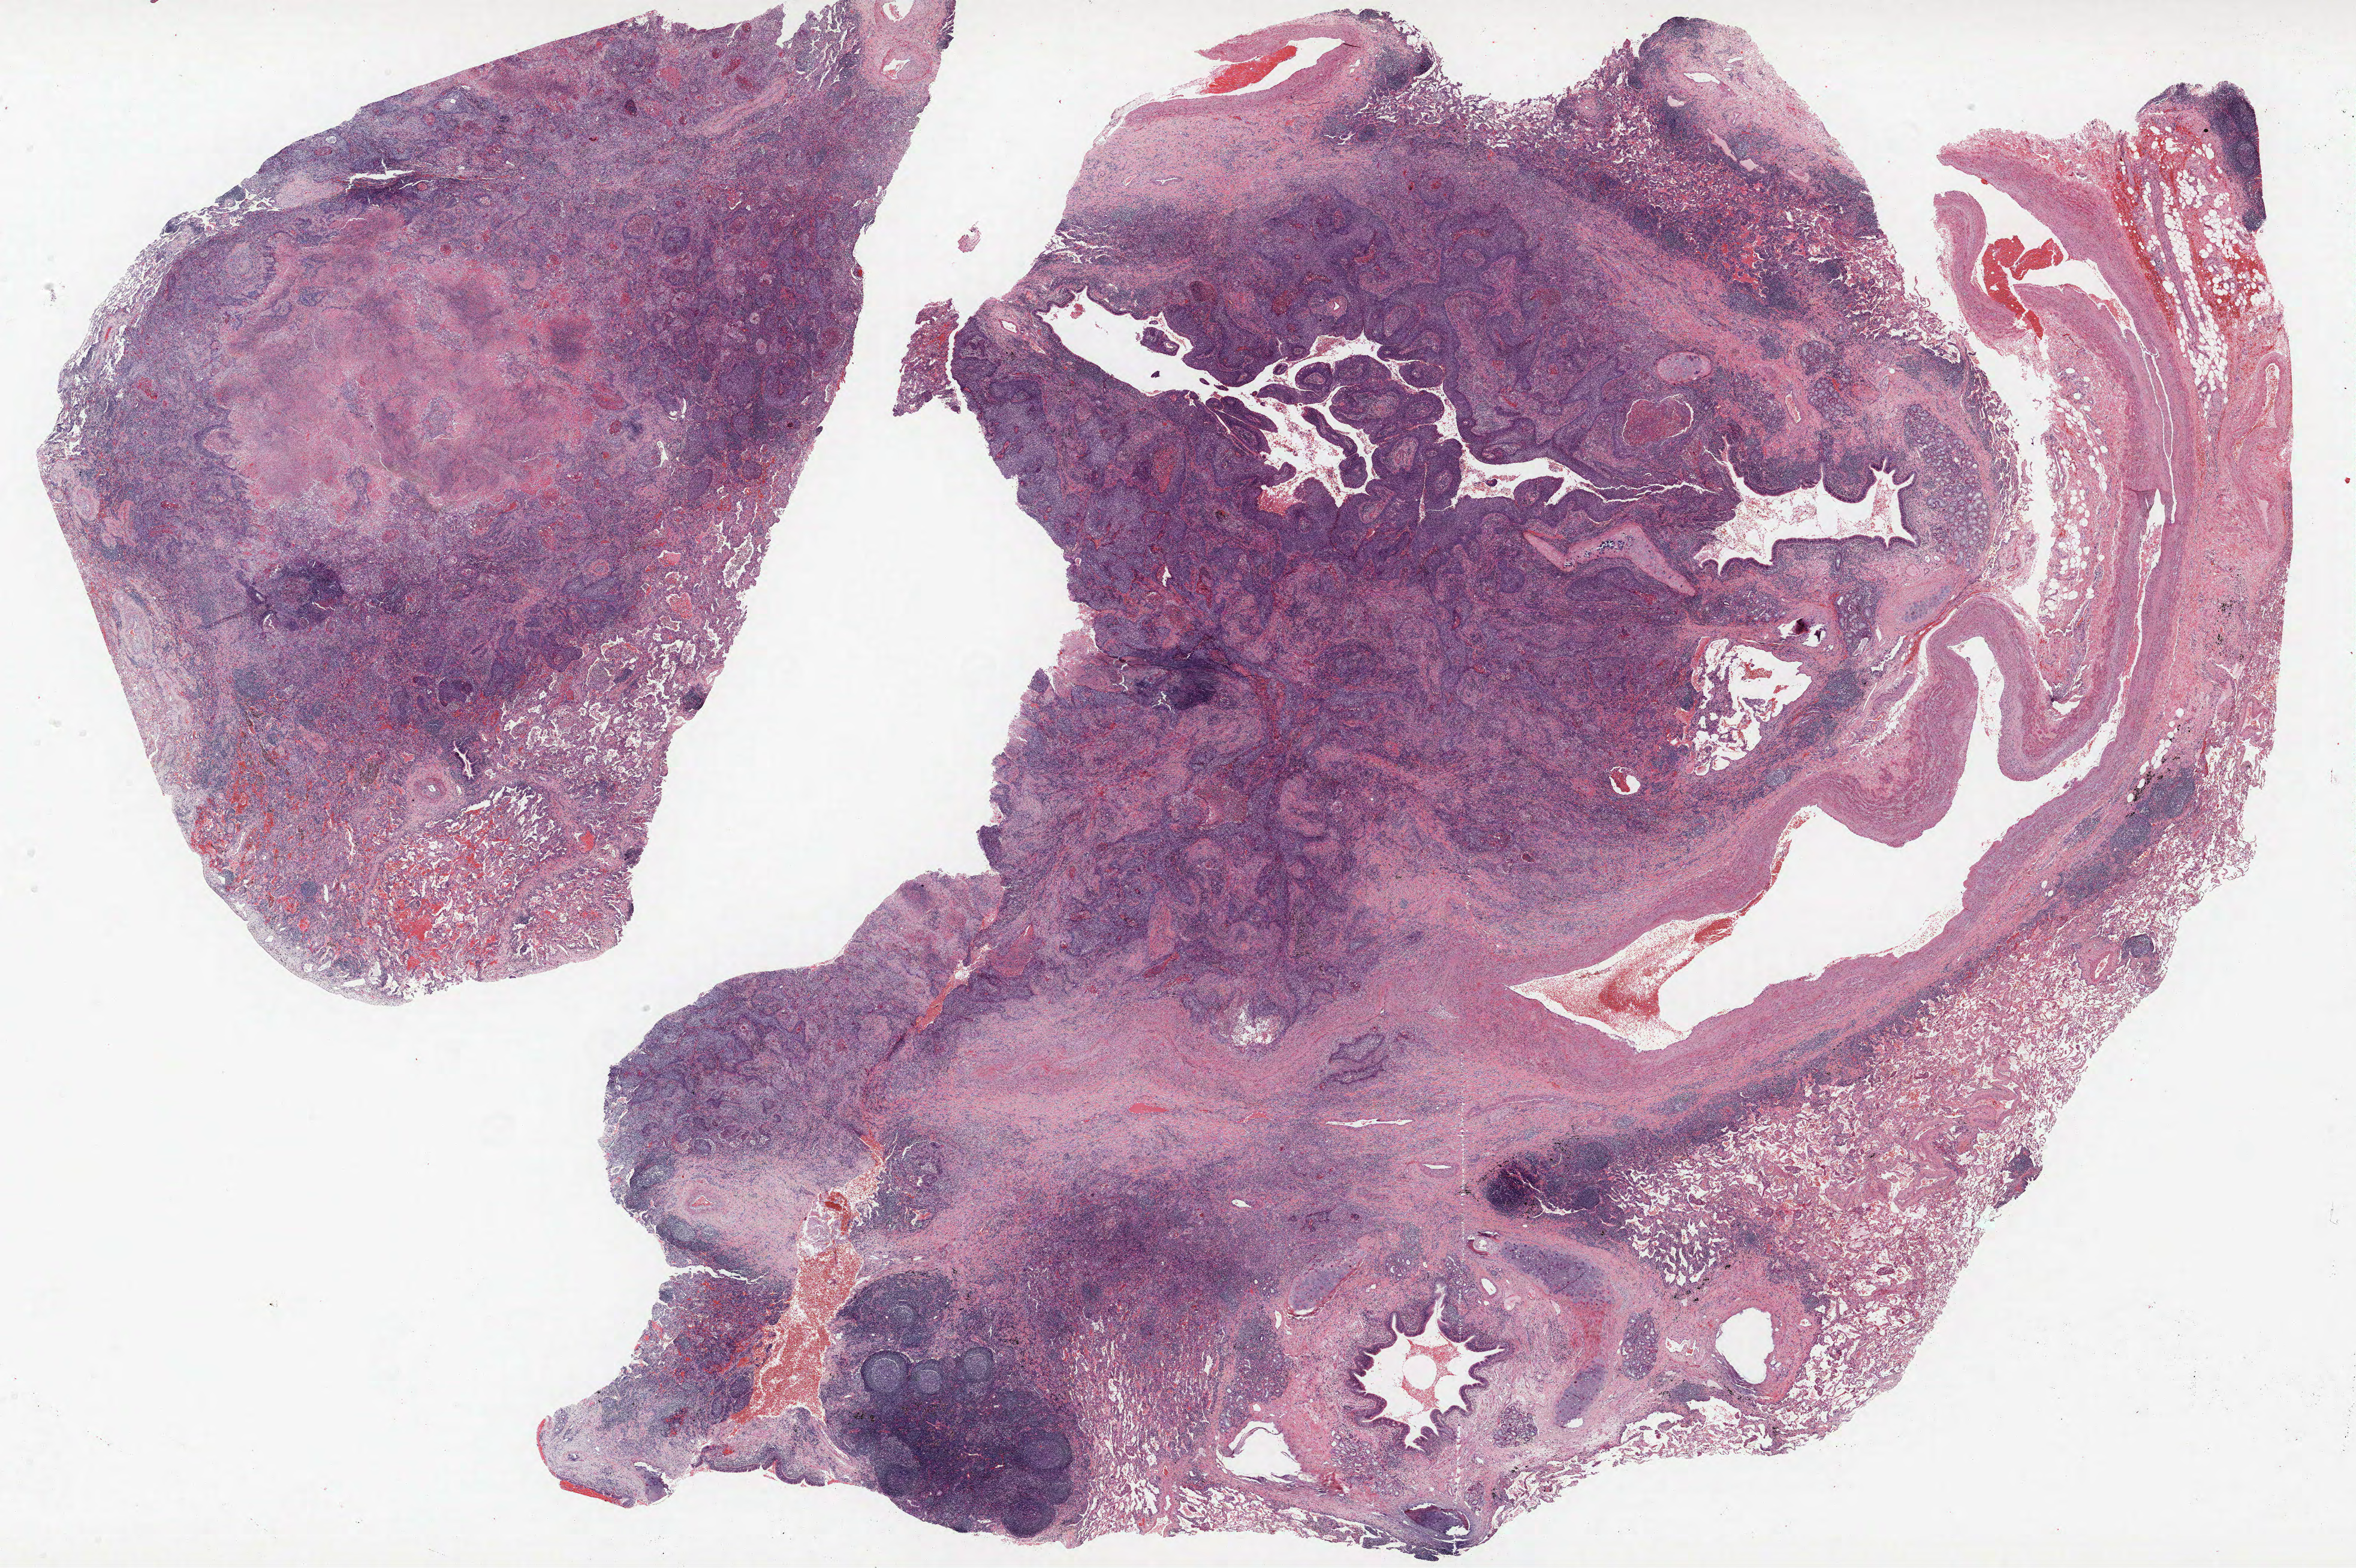
Whole-slide histology image, Hematoxylin and eosin (H&E) stained, whole scanned area (about 31.4 x 20.9 mm, from a 40x scan) shown as a low-resolution overview; formalin-fixed paraffin-embedded (FFPE) section; lung tissue. Male patient, aged 68 at enrolment. Grade: poorly differentiated (G3).
Stage (AJCC 6th edition): IIB. Primary tumour location (clinical record): left lower lobe. Tumour size (pathology): 40 mm. Participant's lung-cancer diagnosis: Squamous cell carcinoma, NOS (ICD-O-3 8070/3).